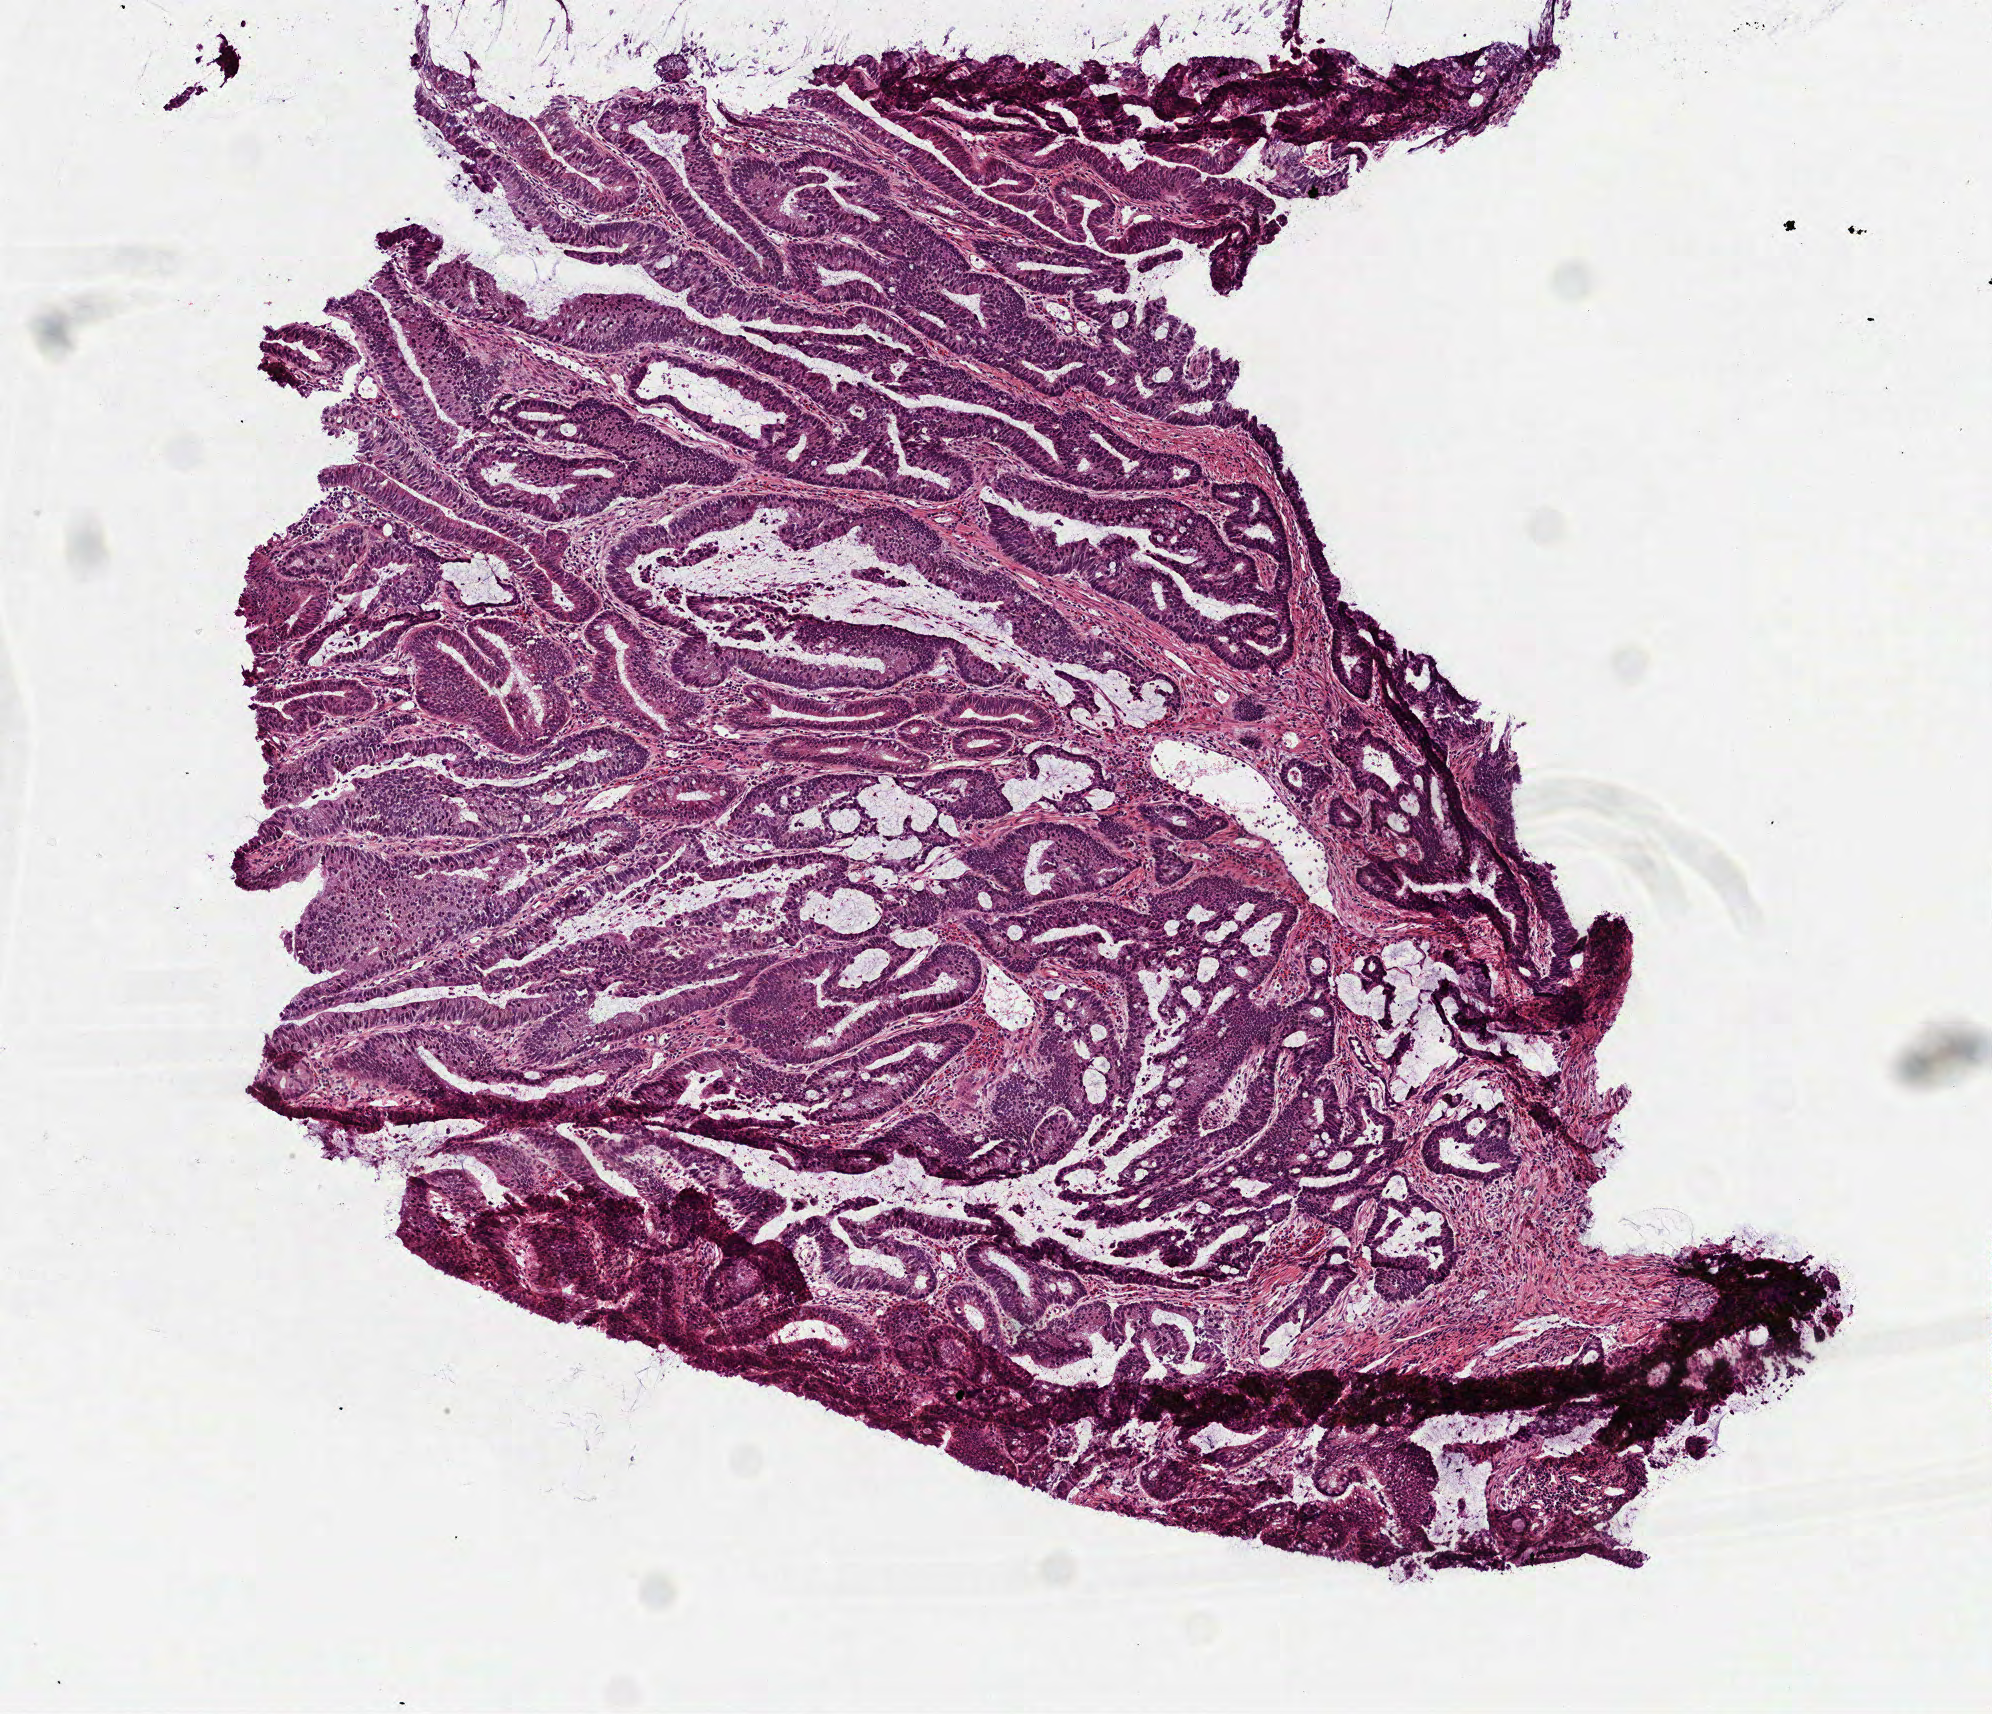
Digitized H&E-stained tissue section (whole slide) — low-resolution overview of the scanned area, about 4.0 x 3.5 mm. Frozen section from the top of the tissue portion. Sample: primary tumour, rectum. Patient: male, age at initial diagnosis 67 years. Composition of this section per pathologist review: tumour cells 100%, tumour nuclei 80%, normal cells 0%, stromal cells 0%, necrosis 0%. Infiltration values recorded for this section: lymphocyte infiltration 5%, monocyte infiltration 1%, neutrophil infiltration 5%.
Lymph nodes positive (case pathology): 1 of 26 examined. AJCC pathologic stage: IIIA. Histologic diagnosis: Mucinous adenocarcinoma (rectosigmoid junction).